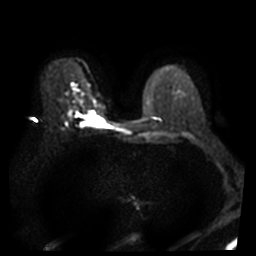
Breast MRI, one axial slice. Position 25 of 46 along the scan axis. Diffusion-weighted series; image 2 of 4 stored at this slice position (different b-values; order by instance number). 3 T. 5 mm slice thickness. 256 × 256 image matrix, field of view 340 × 340 mm. Female patient.
Outlined on this slice (manually delineated by an expert):
- tumour on diffusion-weighted imaging: box from (x=92, y=111) to (x=104, y=125) px